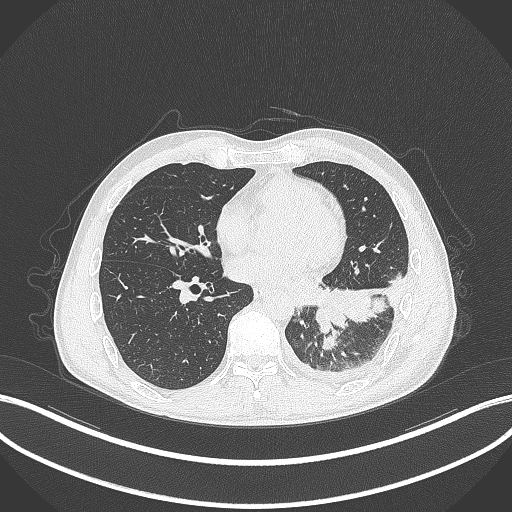
Chest CT, one axial slice; position 128 of 295 along the scan axis; 120 kVp; lung window (W 1500 / L -600 HU); 512 × 512 image matrix. Patient: male, 47 years. From the clinical record (not read from this slice): clinical TNM (as recorded): T3 N1 M1c; histopathological grade: G3.
Outlined on this slice (bounding box drawn by a radiologist):
- lung tumour (recorded histology: small cell carcinoma): bounding box (x1, y1, x2, y2) in pixels: (316, 283, 352, 331)